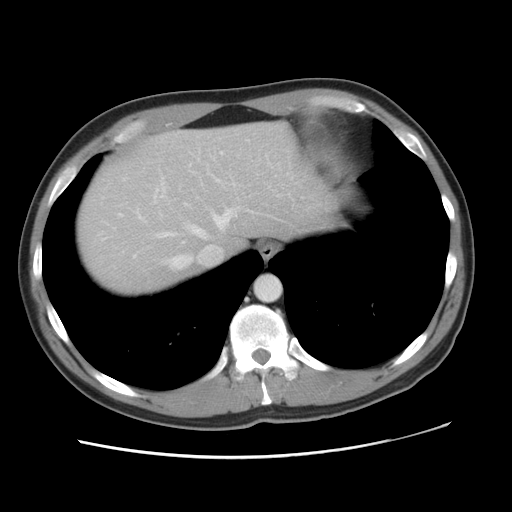
Contrast-enhanced abdominal CT, one axial slice. Slice 41 of 49 in the series (ordered by position). Reconstruction kernel STANDARD. Intravenous contrast given. Soft-tissue window (W 400 / L 40 HU). 5 mm slice thickness. 512 × 512 image matrix, field of view 363 × 363 mm. Male patient, age 41 years. From the clinical record (not read from this slice): diagnosis: colorectal cancer liver metastases, imaged before liver resection; multiple liver metastases: yes.
Structures marked on this image (outlined manually by an expert reader):
- hepatic veins: bounding box (x1, y1, x2, y2) in pixels: (136, 188, 240, 268)
- liver: (76, 124, 309, 296)
- planned liver remnant (the part of the liver to remain after resection): (111, 124, 309, 256)
- portal vein (with intrahepatic branches): (119, 152, 222, 215)